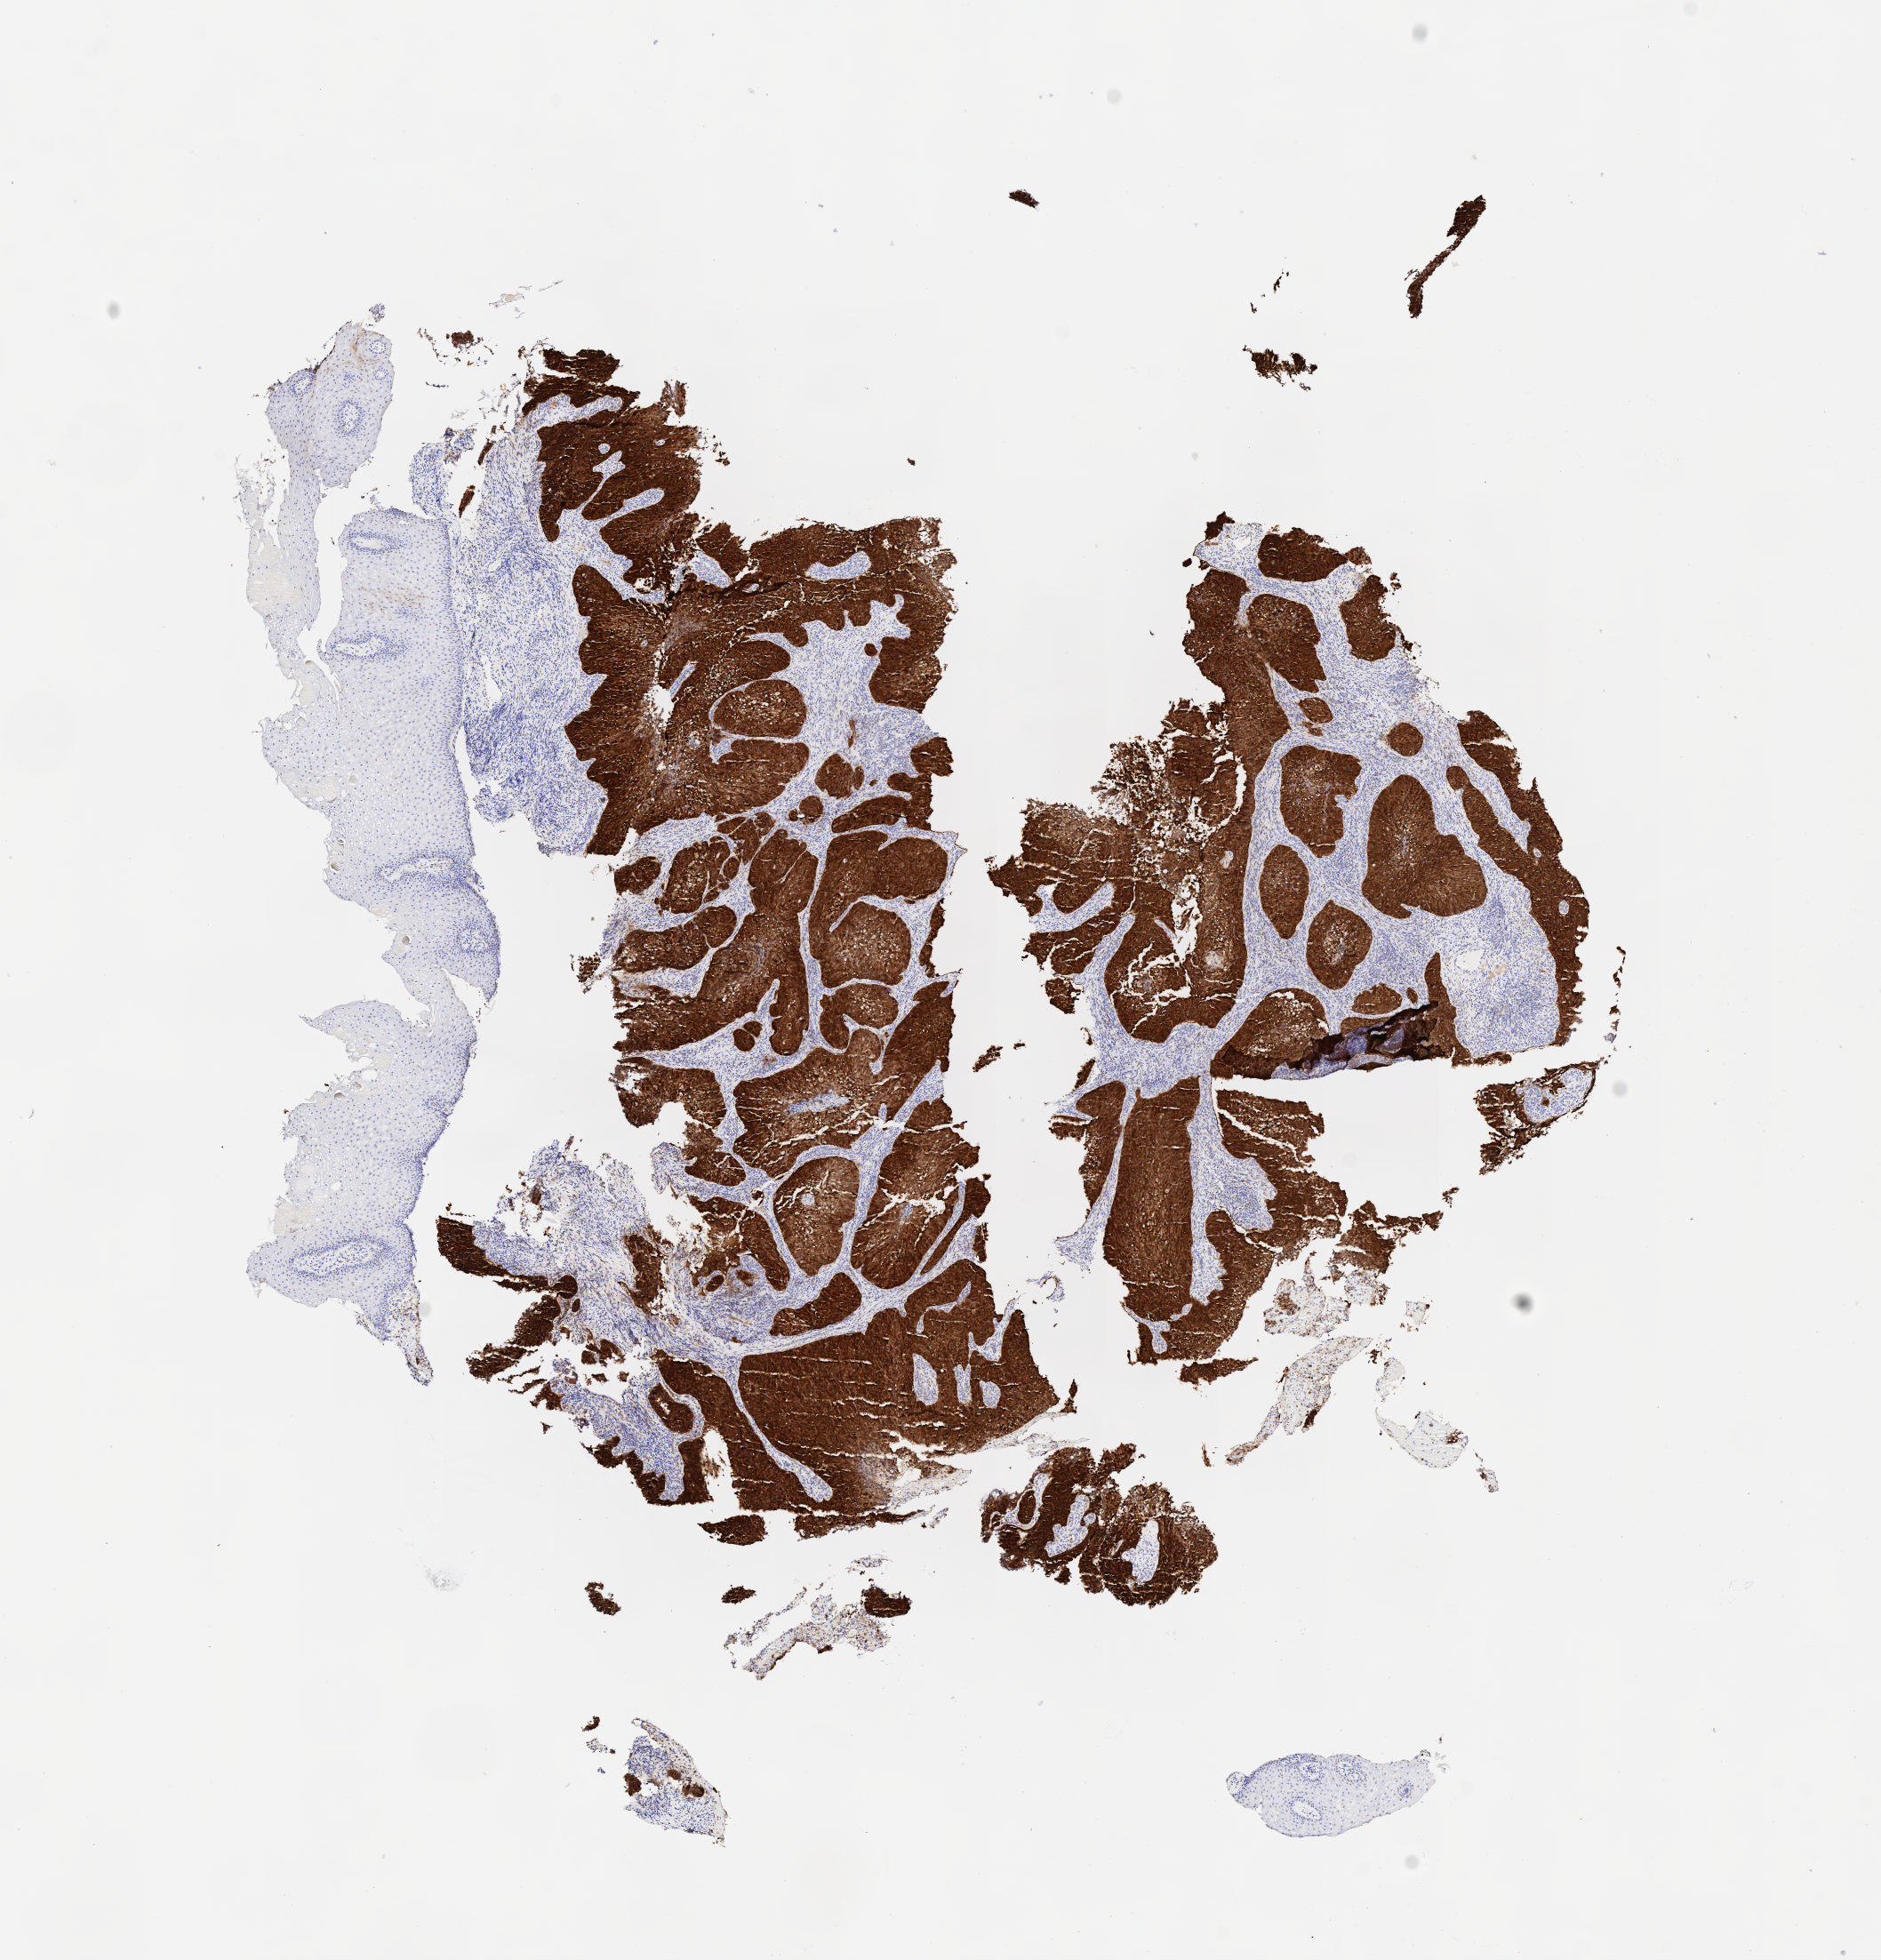
Whole-slide image, immunohistochemical stain for p16 (p16INK4a), whole scanned area (about 8.6 x 8.9 mm) shown as a low-resolution overview; tumor tissue; anatomic site: cervix. Patient female; age 33 years.
Histologic diagnosis: Squamous cell carcinoma, large cell, nonkeratinizing, NOS.